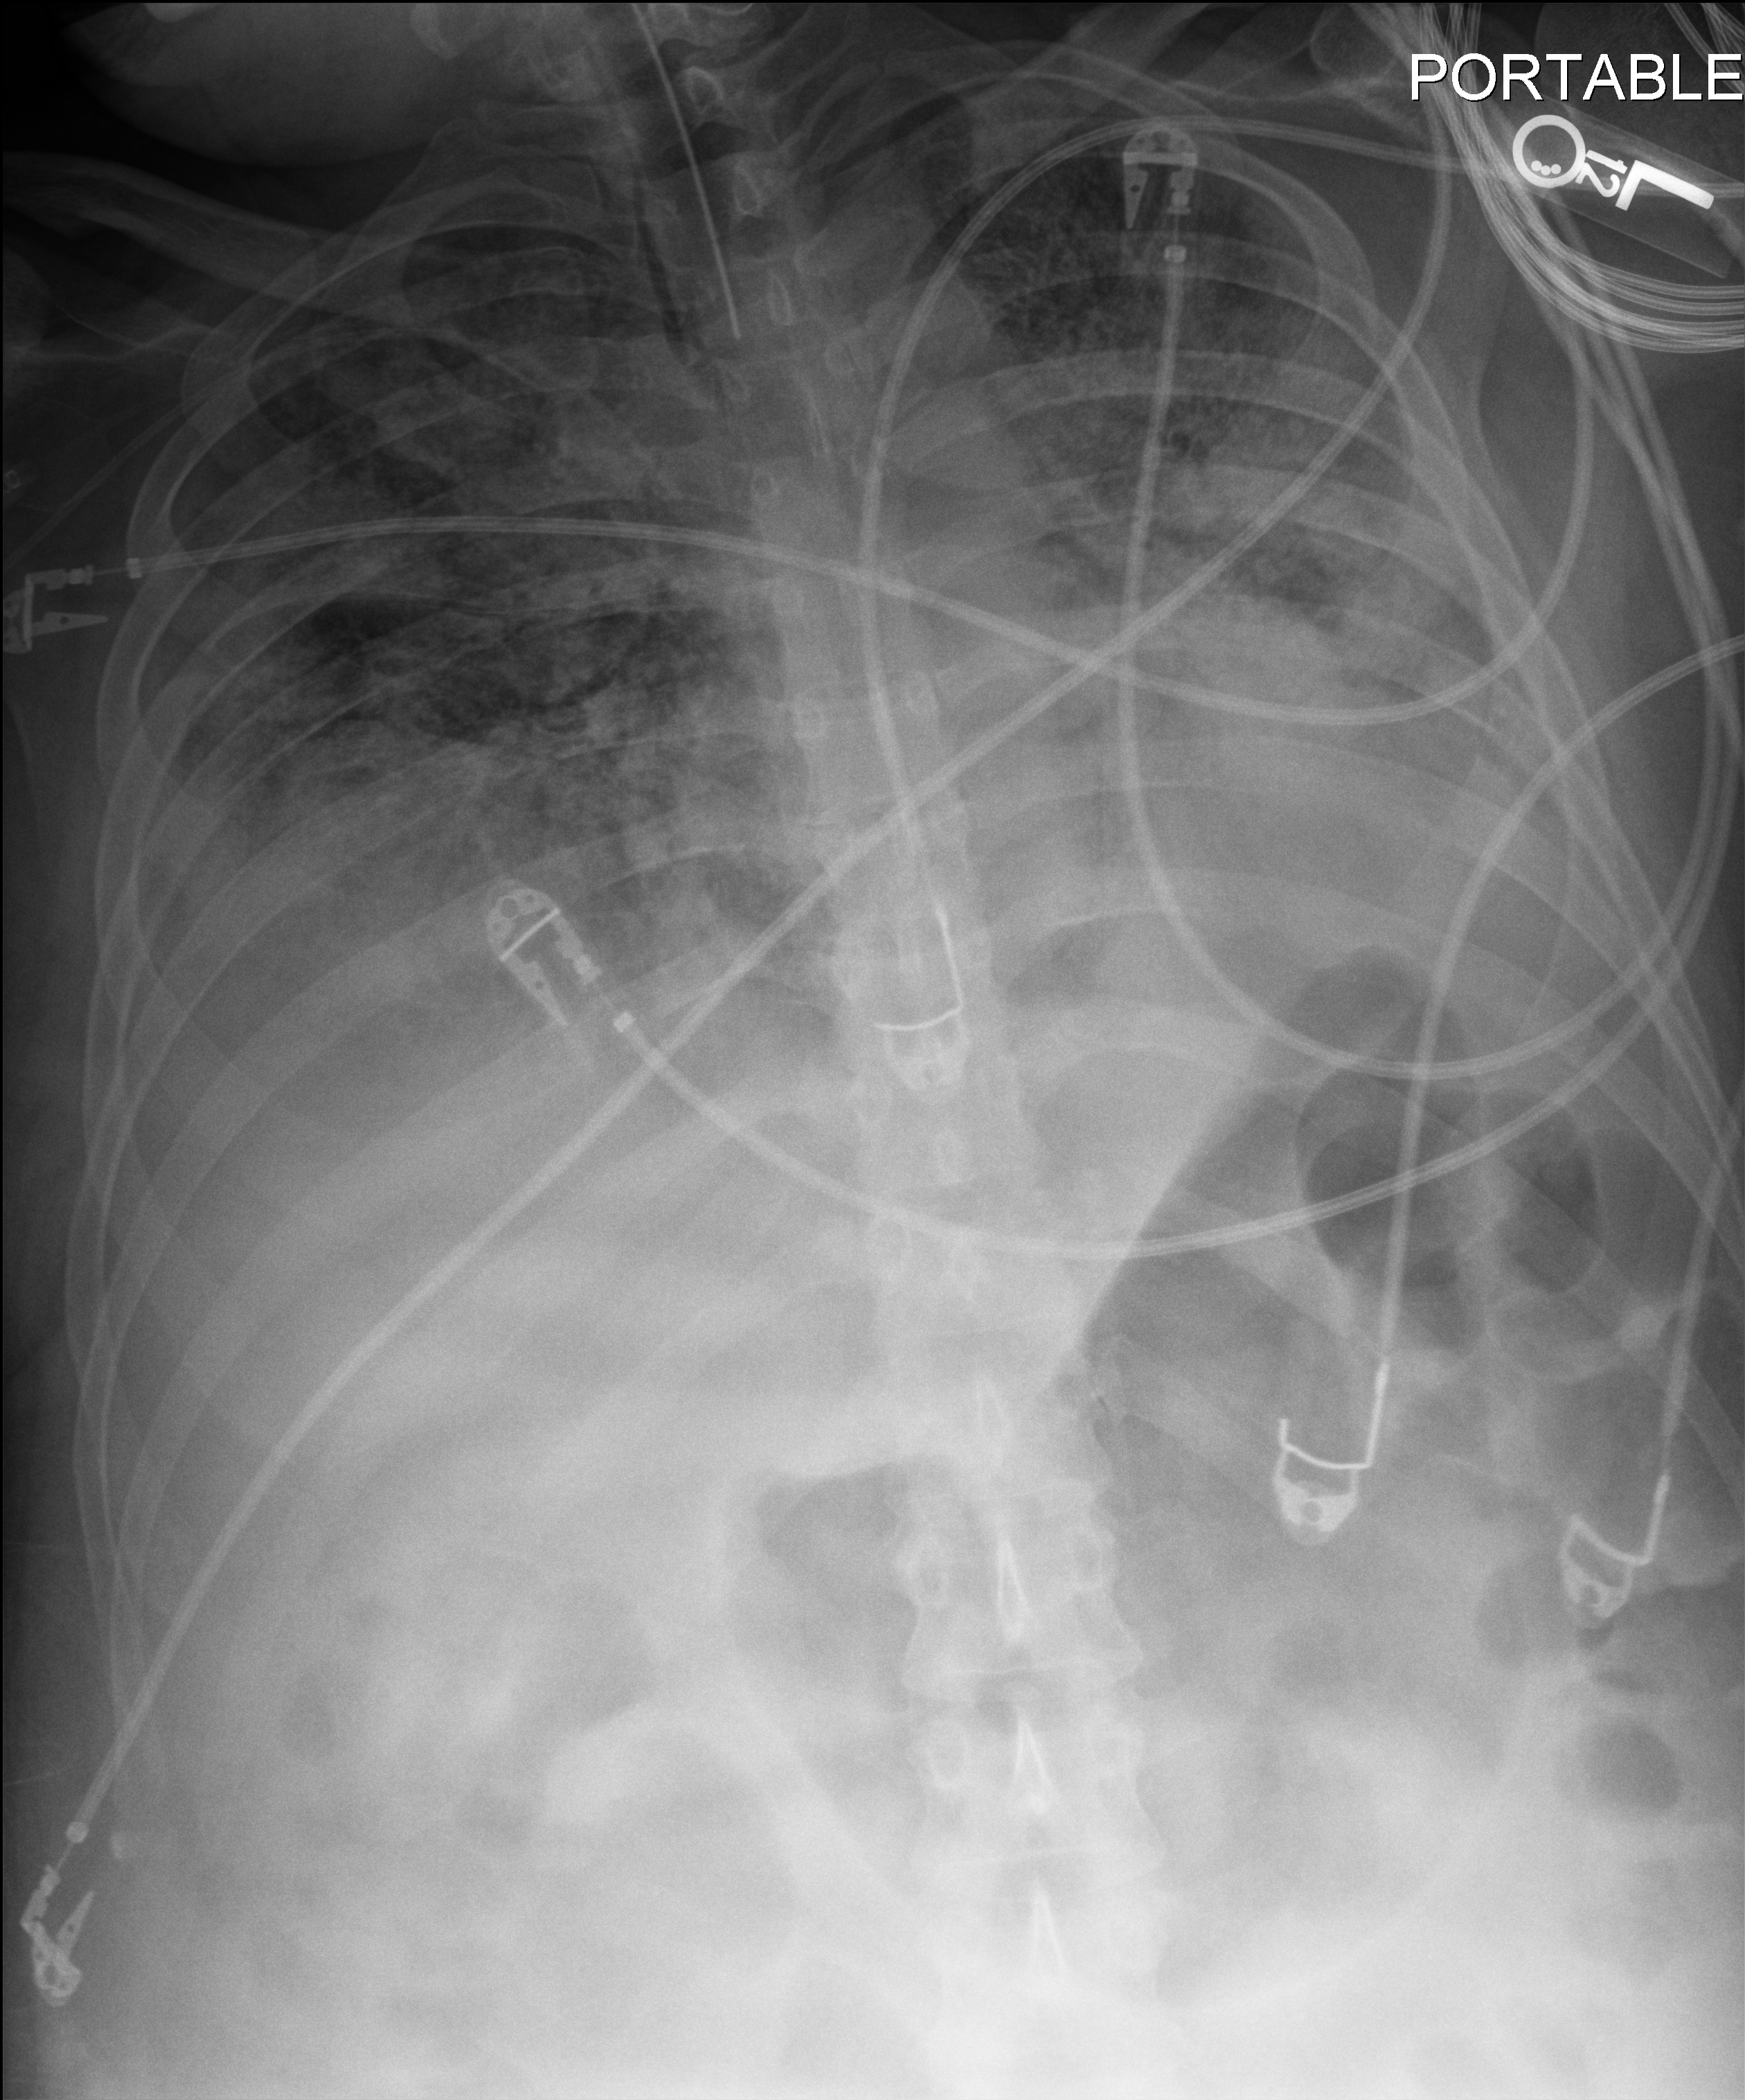
Chest X-ray (portable), anteroposterior (AP) projection. Male patient hospitalised with COVID-19, age 18–59 years.
From the hospital-stay record, not from the radiograph (when in the stay this image was taken is not recorded): COPD (admission record): no; mechanically ventilated during this hospital stay: yes; length of hospital stay: 96 days.